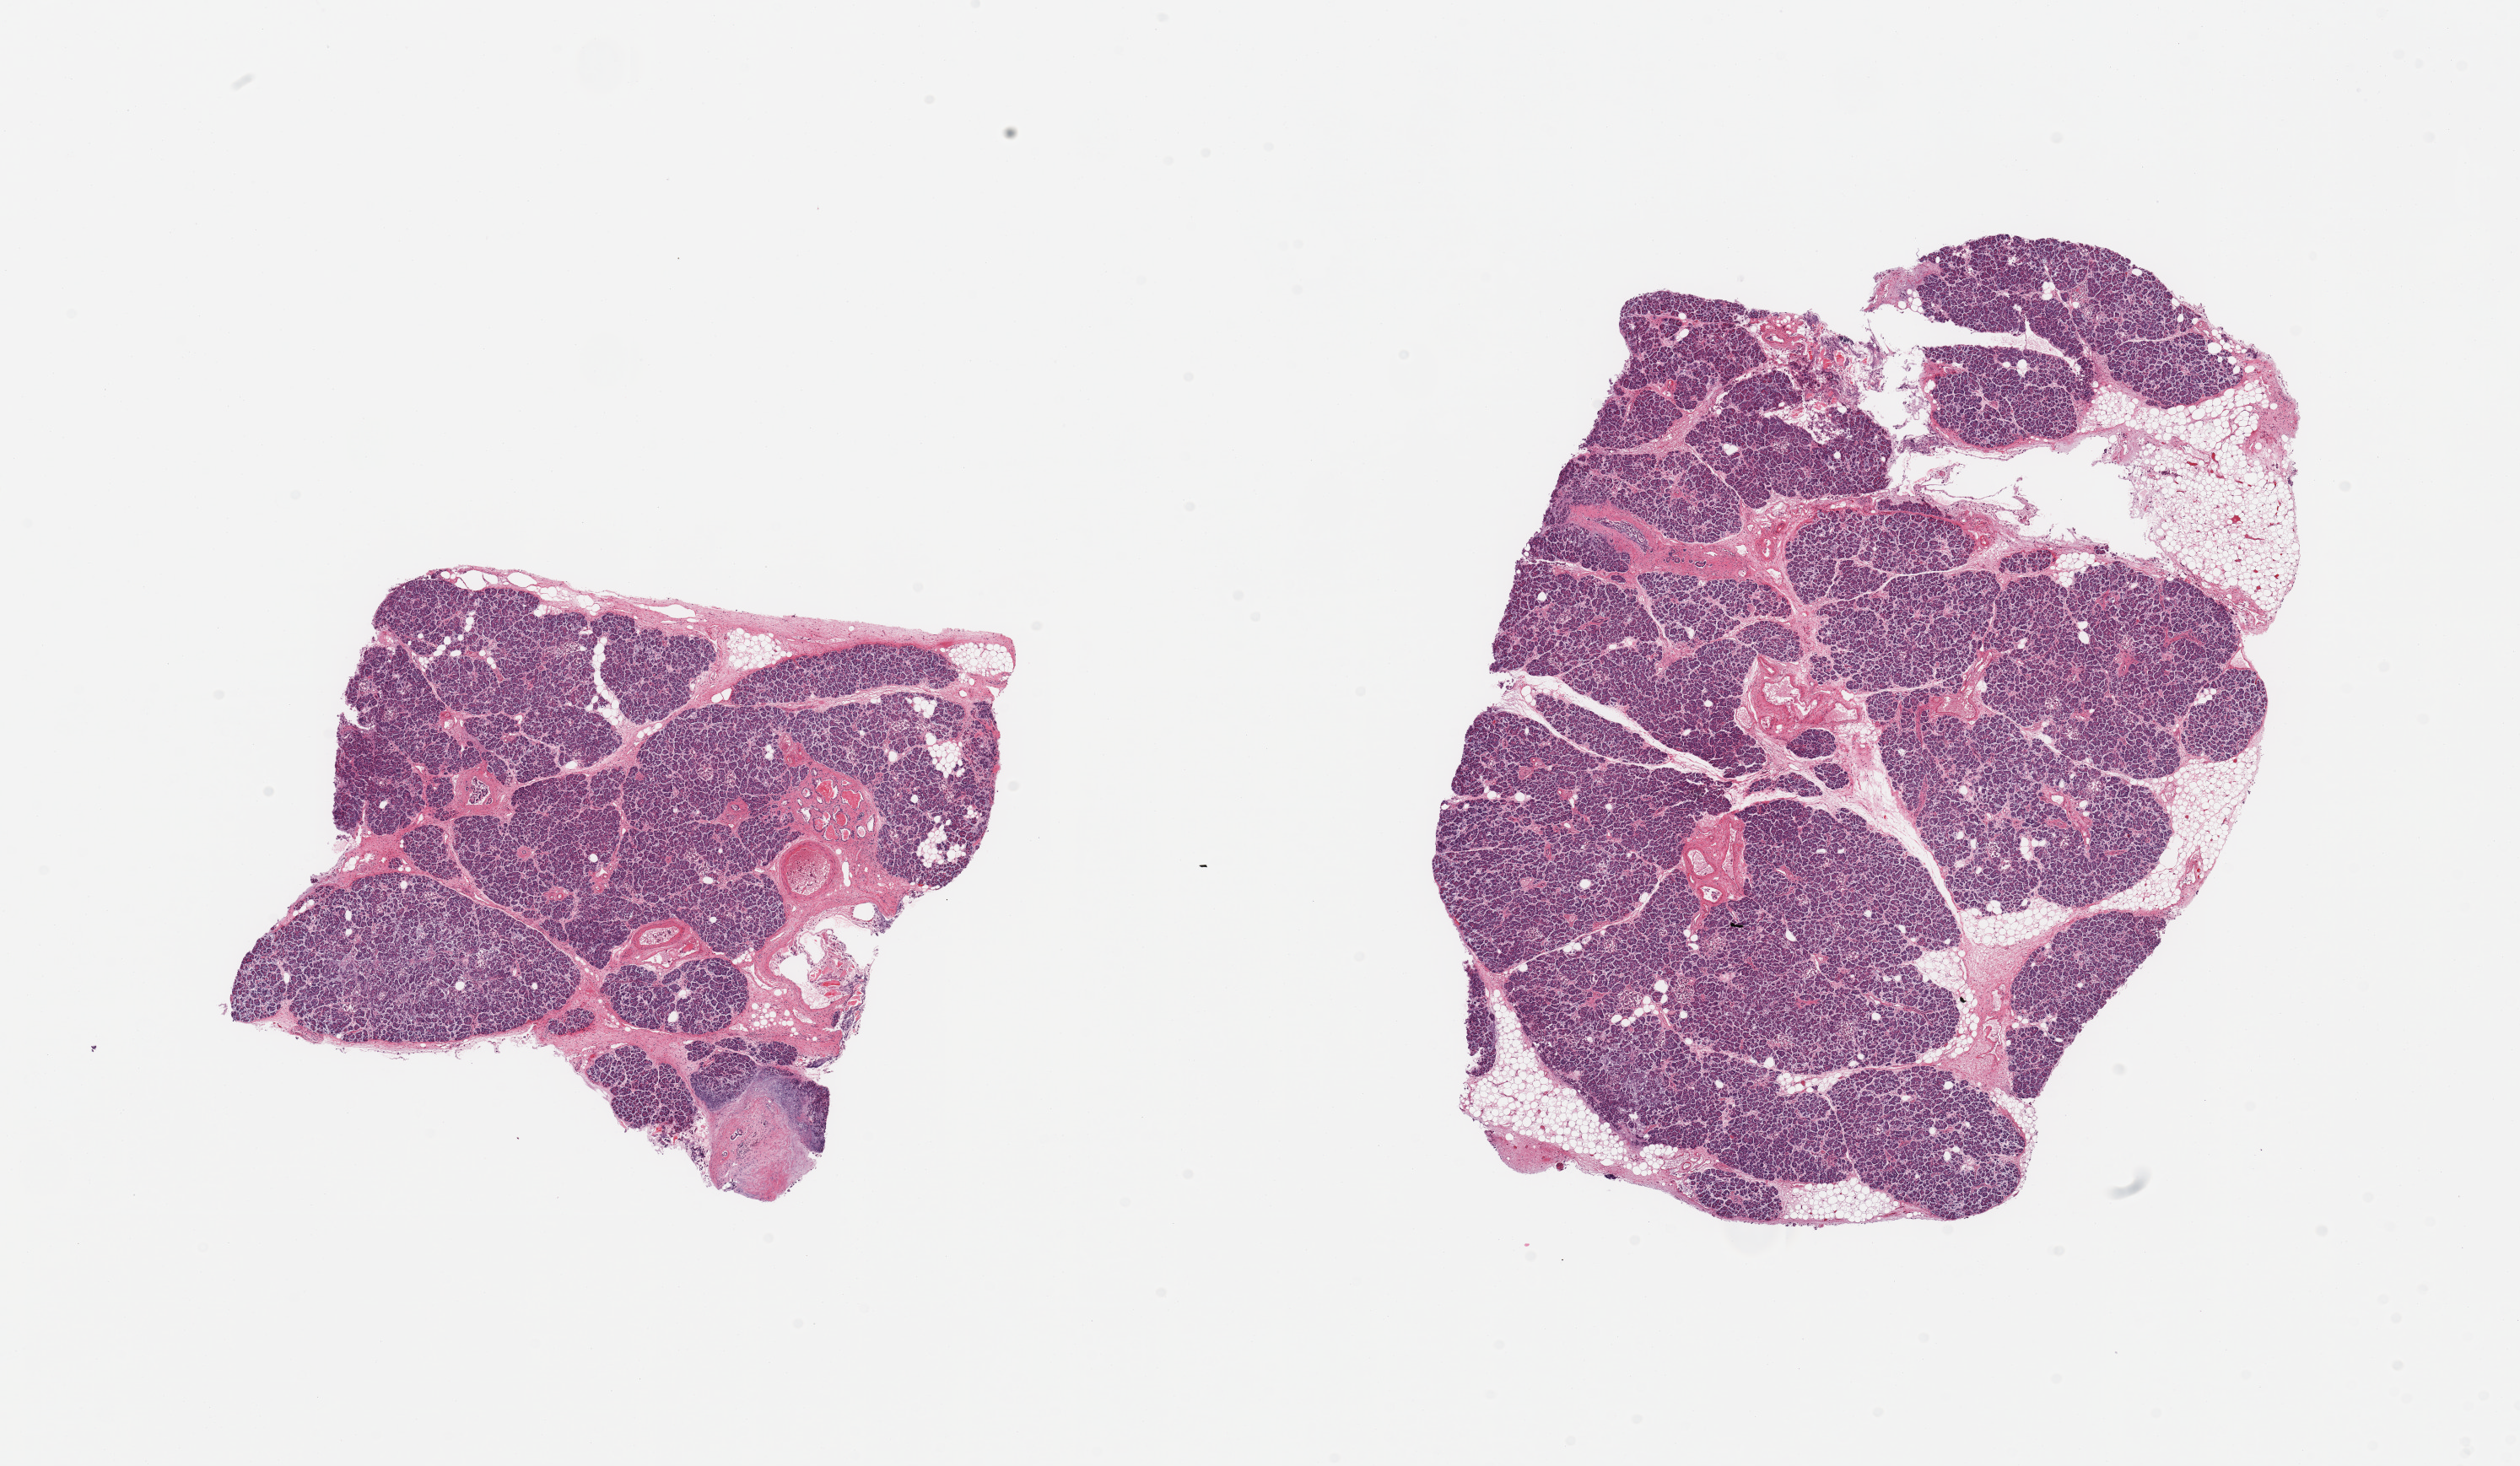
Digitized haematoxylin and eosin-stained section, whole scanned area (about 23.6 x 13.7 mm, slide scanned at 20x) shown as a low-resolution overview; PAXgene-fixed, paraffin-embedded tissue; sampled site (target tissue): pancreas; tissue donor sample. Donor: male.
- pathologist's review note for this sample: 2 pieces; several foci (10%) of periductal fibrosis; 10% adipose